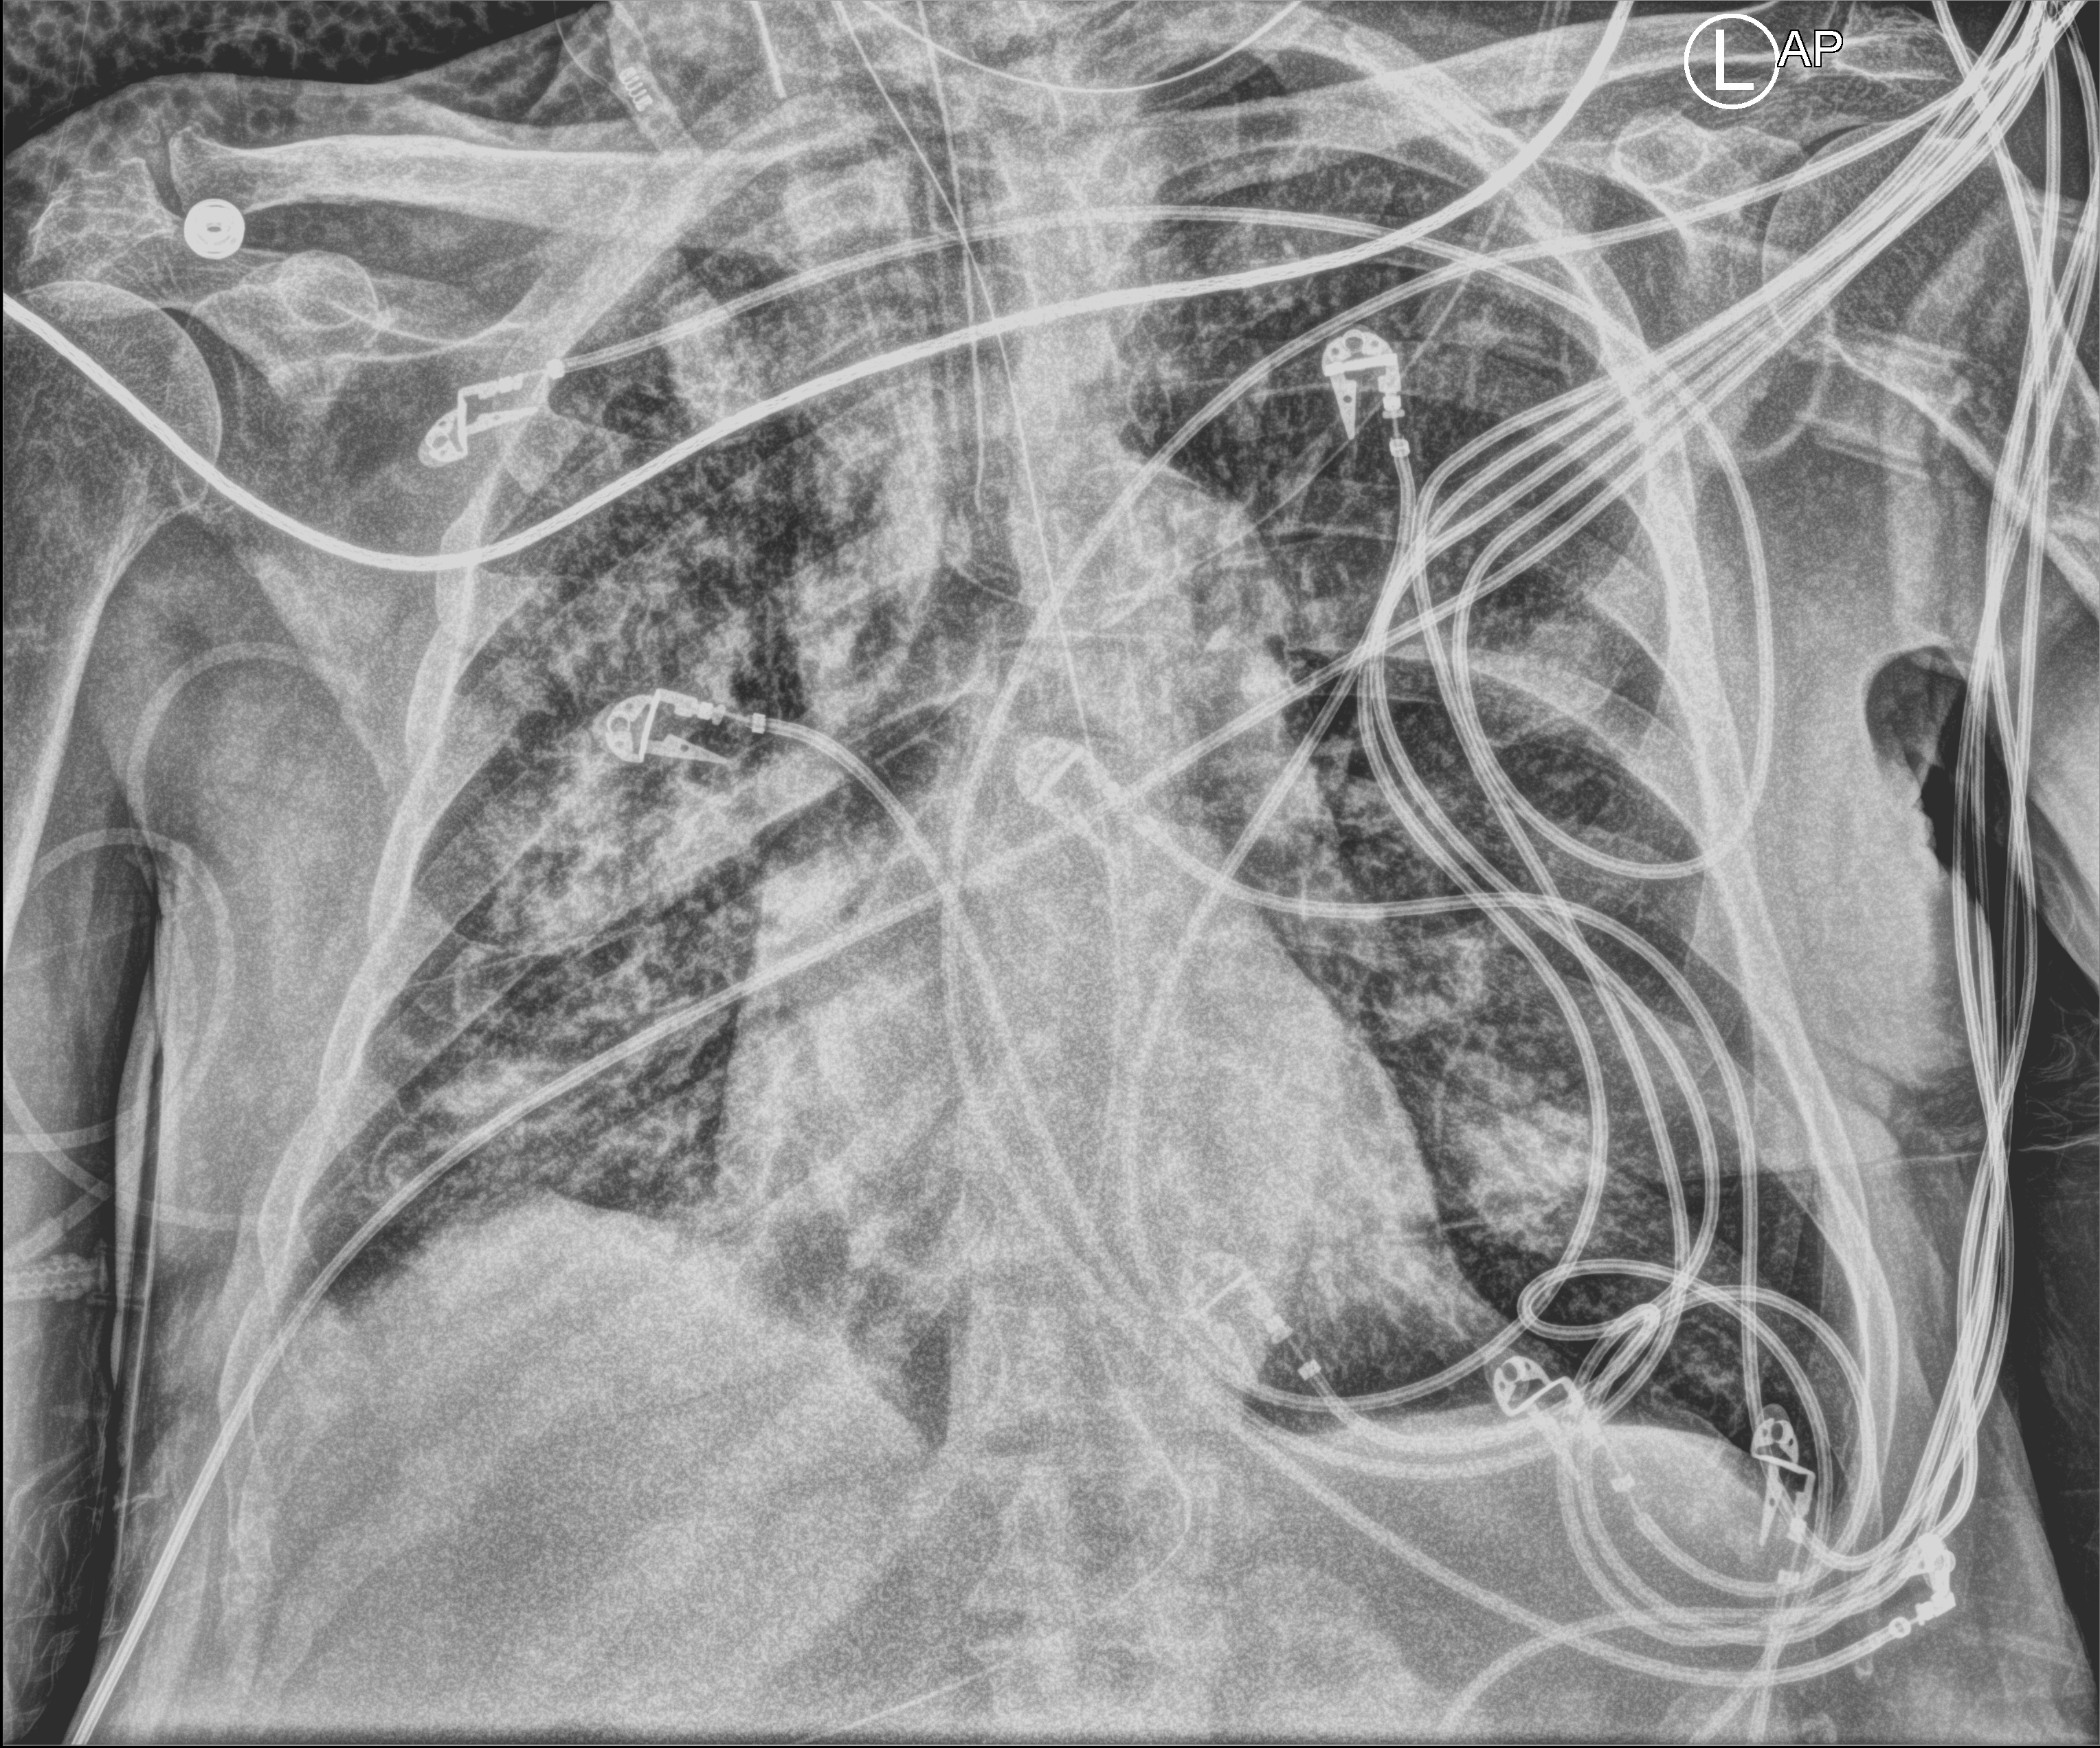
Bedside chest radiograph (computed radiography), anteroposterior (AP) projection. Male patient hospitalised with COVID-19, age 75–90 years.
Admission-level facts for this patient (not findings on this image; timing relative to this image not recorded): admitted to intensive care during this hospital stay: yes; hypertension (admission record): yes; COPD (admission record): no.